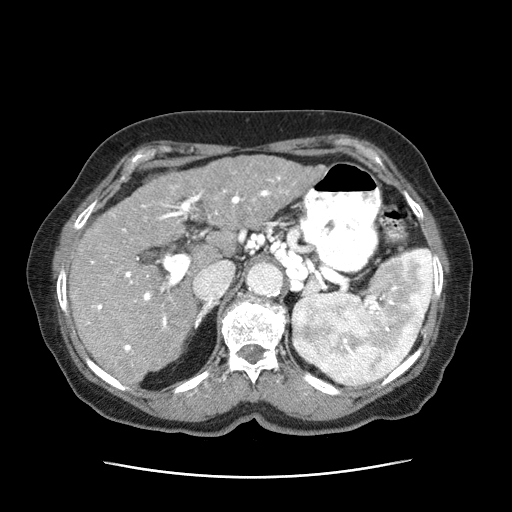
Contrast-enhanced abdominal CT (liver protocol), one axial slice; slice 39 of 63 in the series (ordered by position); reconstruction kernel STANDARD; intravenous contrast given; soft-tissue window (W 400 / L 40 HU); 2.5 mm slice thickness; 512 × 512 image matrix, field of view 360 × 360 mm. Female patient, age 79 years. Case-level facts recorded for this patient, not image findings: diagnosis: hepatocellular carcinoma (patient treated with transarterial chemoembolisation; whether this scan precedes or follows treatment is not stated here); TNM stage (as recorded): Stage-II; Child-Pugh class: B; tumour differentiation: well differentiated.
Outlined on this slice (semi-automatically segmented with operator editing):
- abdominal aorta: bounding box <247,264,283,298> (left, top, right, bottom; pixels)
- liver parenchyma outside the tumour (the mass and vessels are separate outlines, so this box may not span the whole liver): <68,178,239,385>
- mass: <153,156,324,230>
- liver vessels: <78,176,289,366>